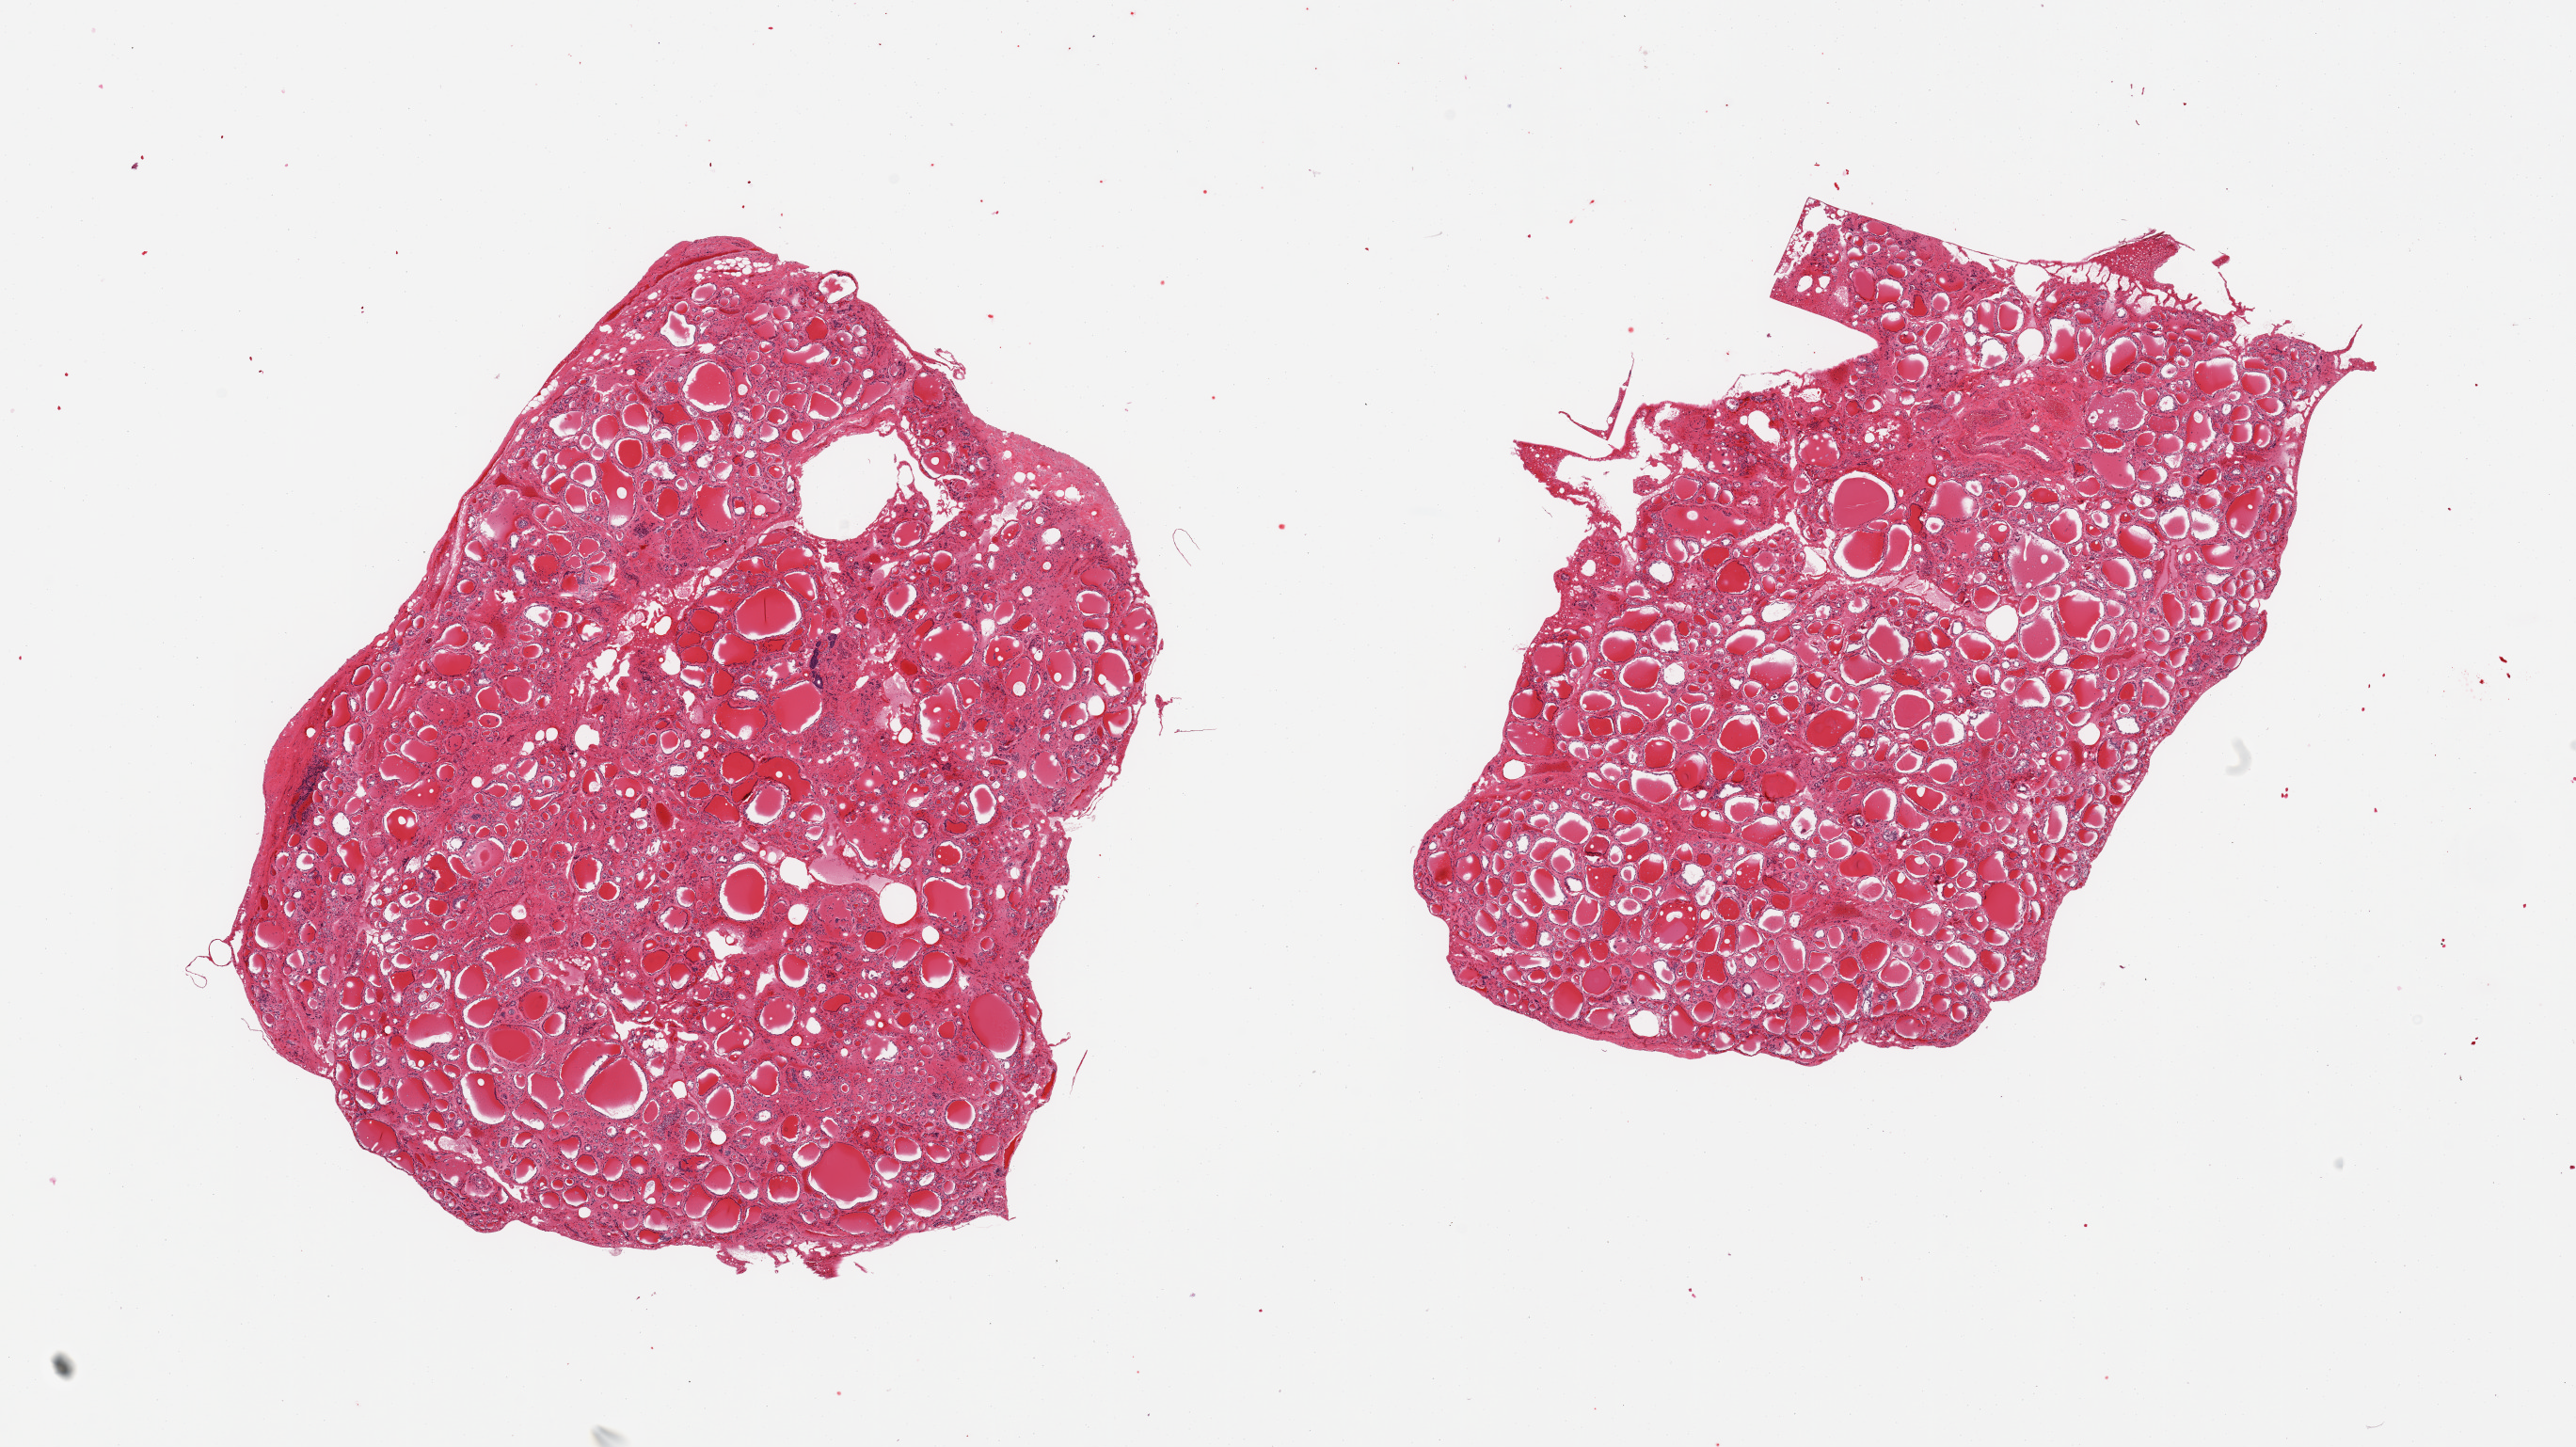
Digitized H&E-stained section — whole scanned area (about 21.7 x 12.2 mm) shown as a low-resolution overview. PAXgene-fixed paraffin-embedded (PFPE) section. Target tissue: thyroid. Tissue donor sample. Male donor.
Reviewer comment on this tissue sample: 2 pieces; mild interstitial fibrosis.